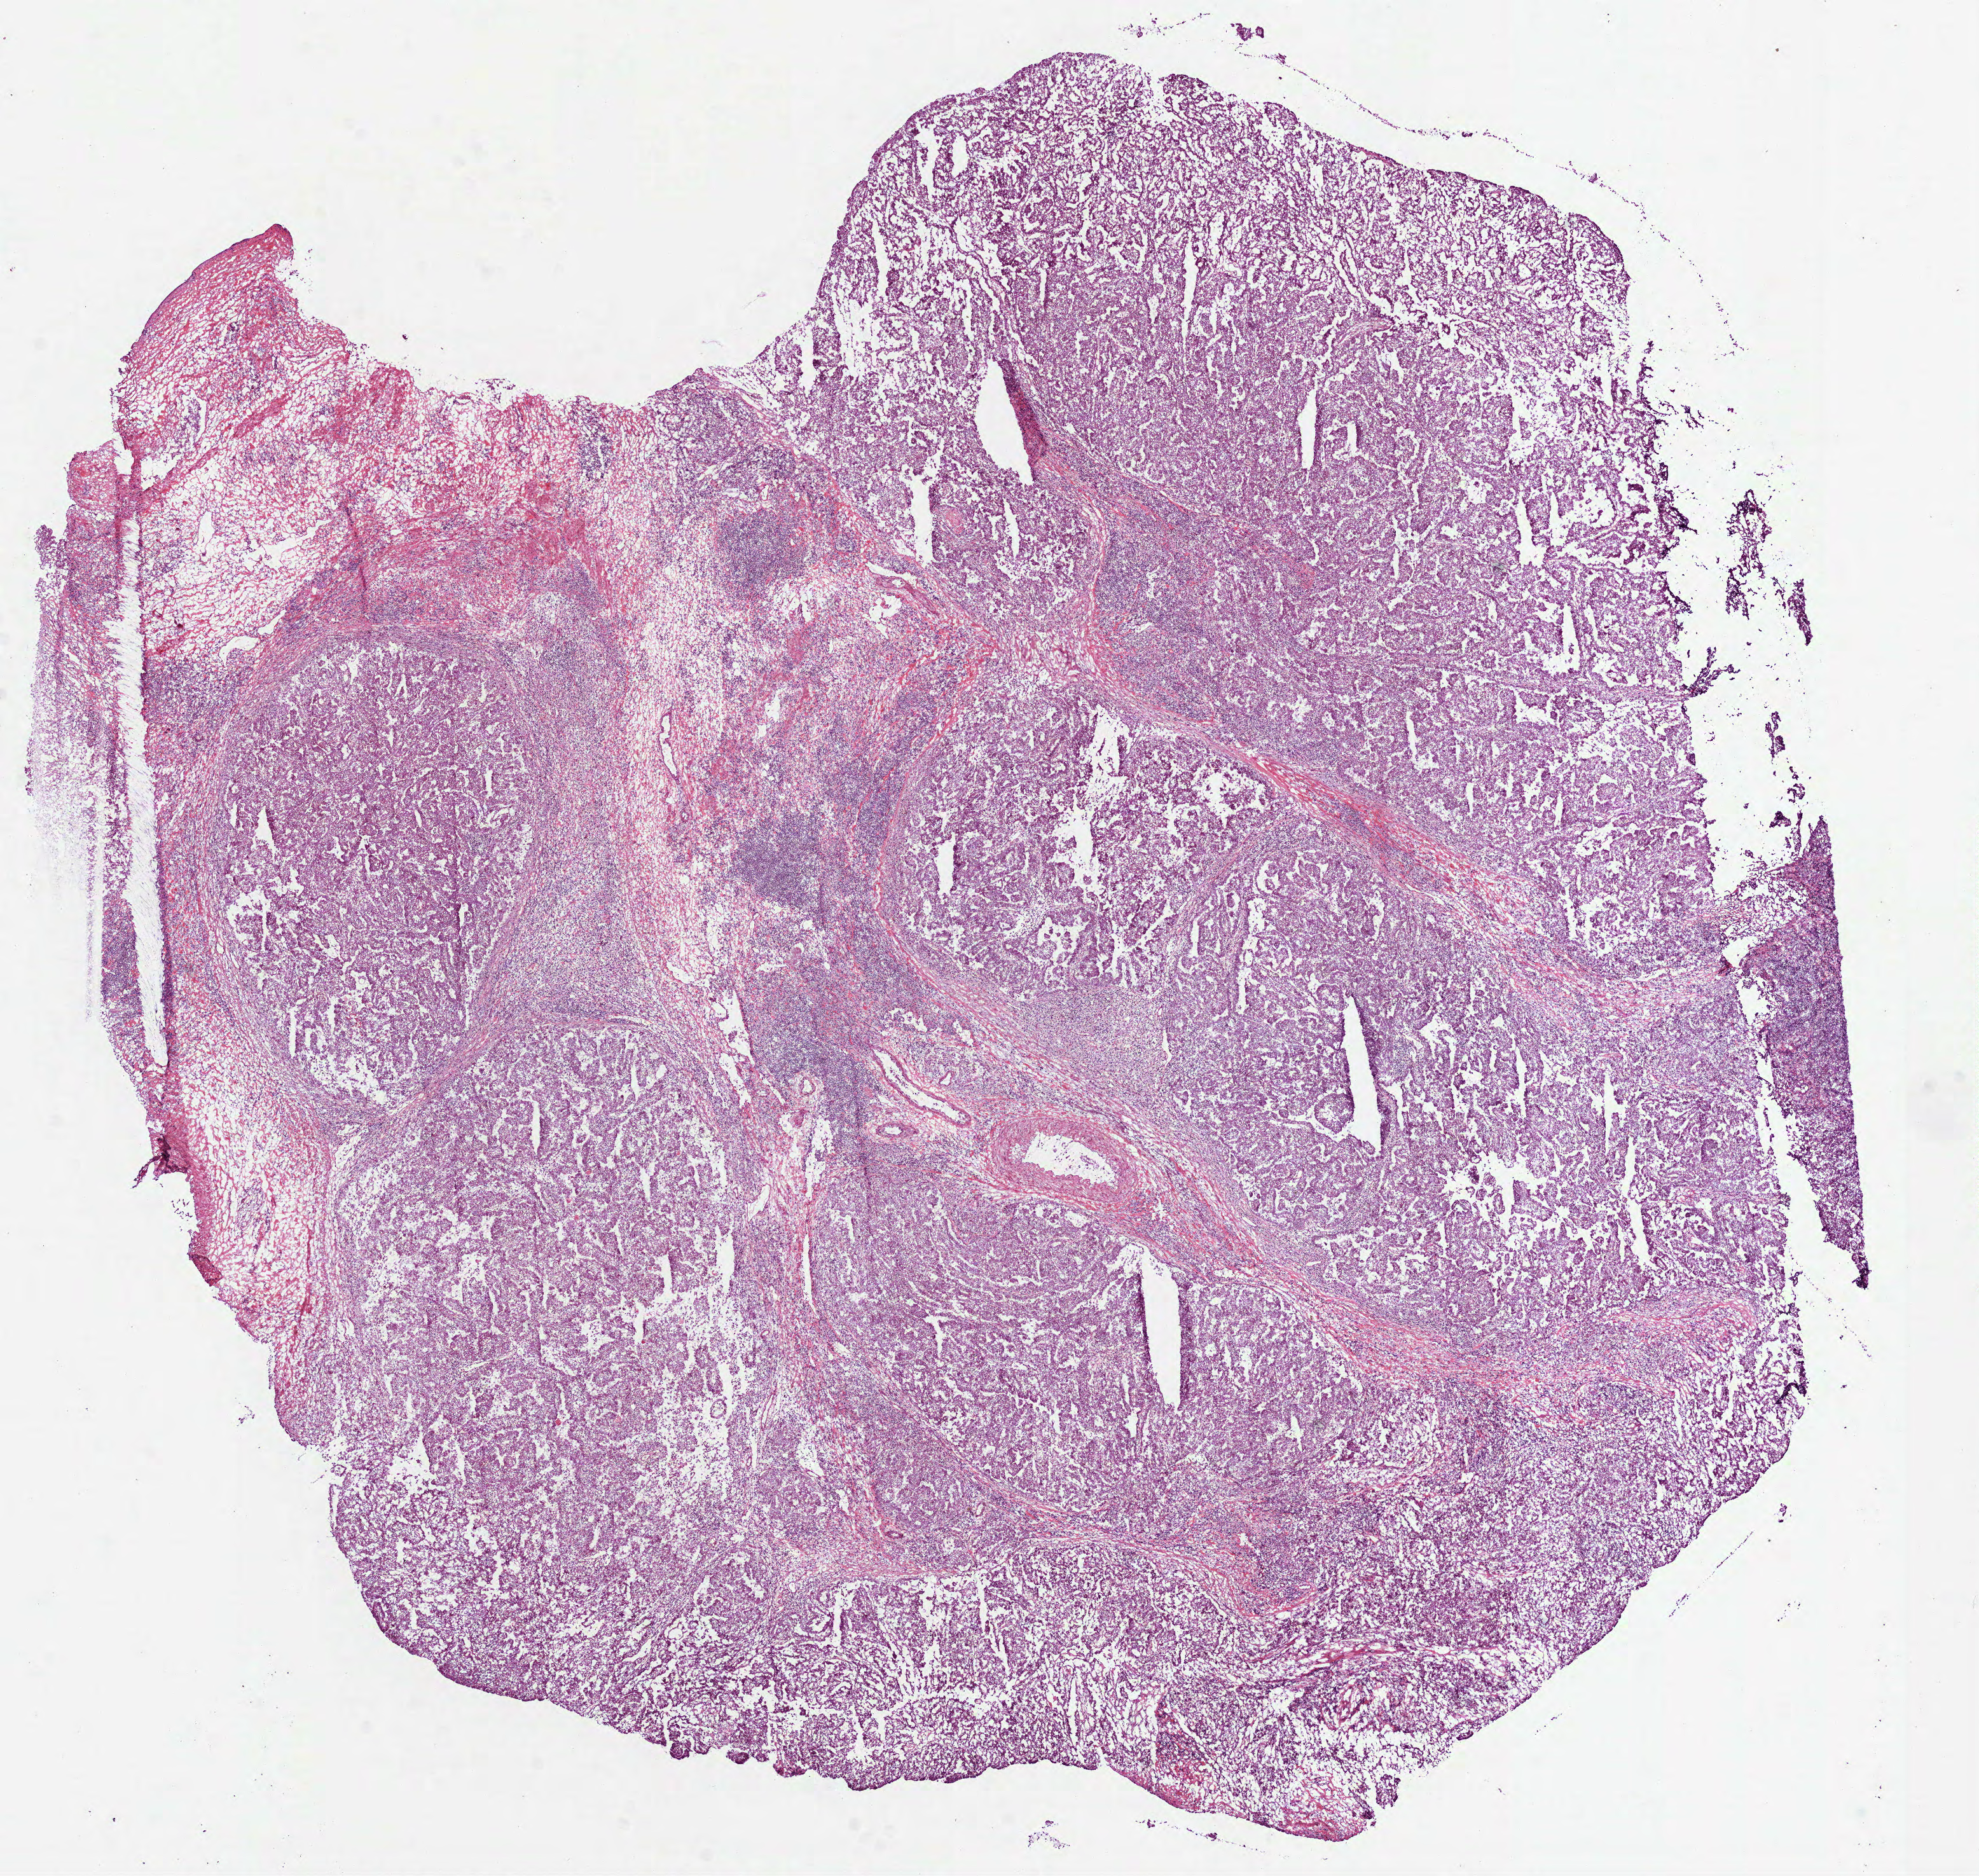
H&E whole-slide image, shown as a low-resolution overview of the whole scanned area (about 12.5 x 11.9 mm, slide scanned at 40x); frozen section from the bottom of the tissue portion; primary tumour sample from the kidney. Female patient; age at initial diagnosis 37 years. Composition of this section per pathologist review: tumour cells 90%, tumour nuclei 70%, normal cells 0%, stromal cells 10%, necrosis 0%.
* pathologic diagnosis: Papillary adenocarcinoma, NOS
* AJCC pathologic stage: III
* laterality: left